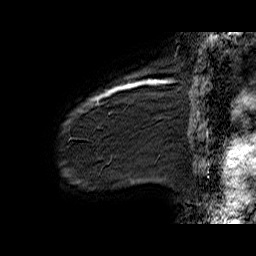
Breast MRI (dynamic contrast-enhanced), one sagittal slice; position 8 of 60 along the scan axis; dynamic contrast-enhanced series, time point 2 of 6 at this slice position (early post-contrast); 1.5 T; TE 6.4 ms, TR 32.9 ms; 4 mm slice thickness; 256 × 256 image matrix, field of view 200 × 200 mm. Female patient. Case-level facts recorded for this patient, not image findings: setting: breast cancer imaged before/during neoadjuvant chemotherapy; receptor status: HER2-positive.
Structures marked on this image (semi-automatically segmented with operator editing):
- analysis volume of interest (the breast-tissue region the enhancement analysis was run in; not a lesion): bounding box [x1, y1, x2, y2] px = [63, 77, 141, 142]
- tumour enhancement mask (voxels above the 100 % enhancement threshold inside the analysis volume of interest): [90, 81, 141, 104]